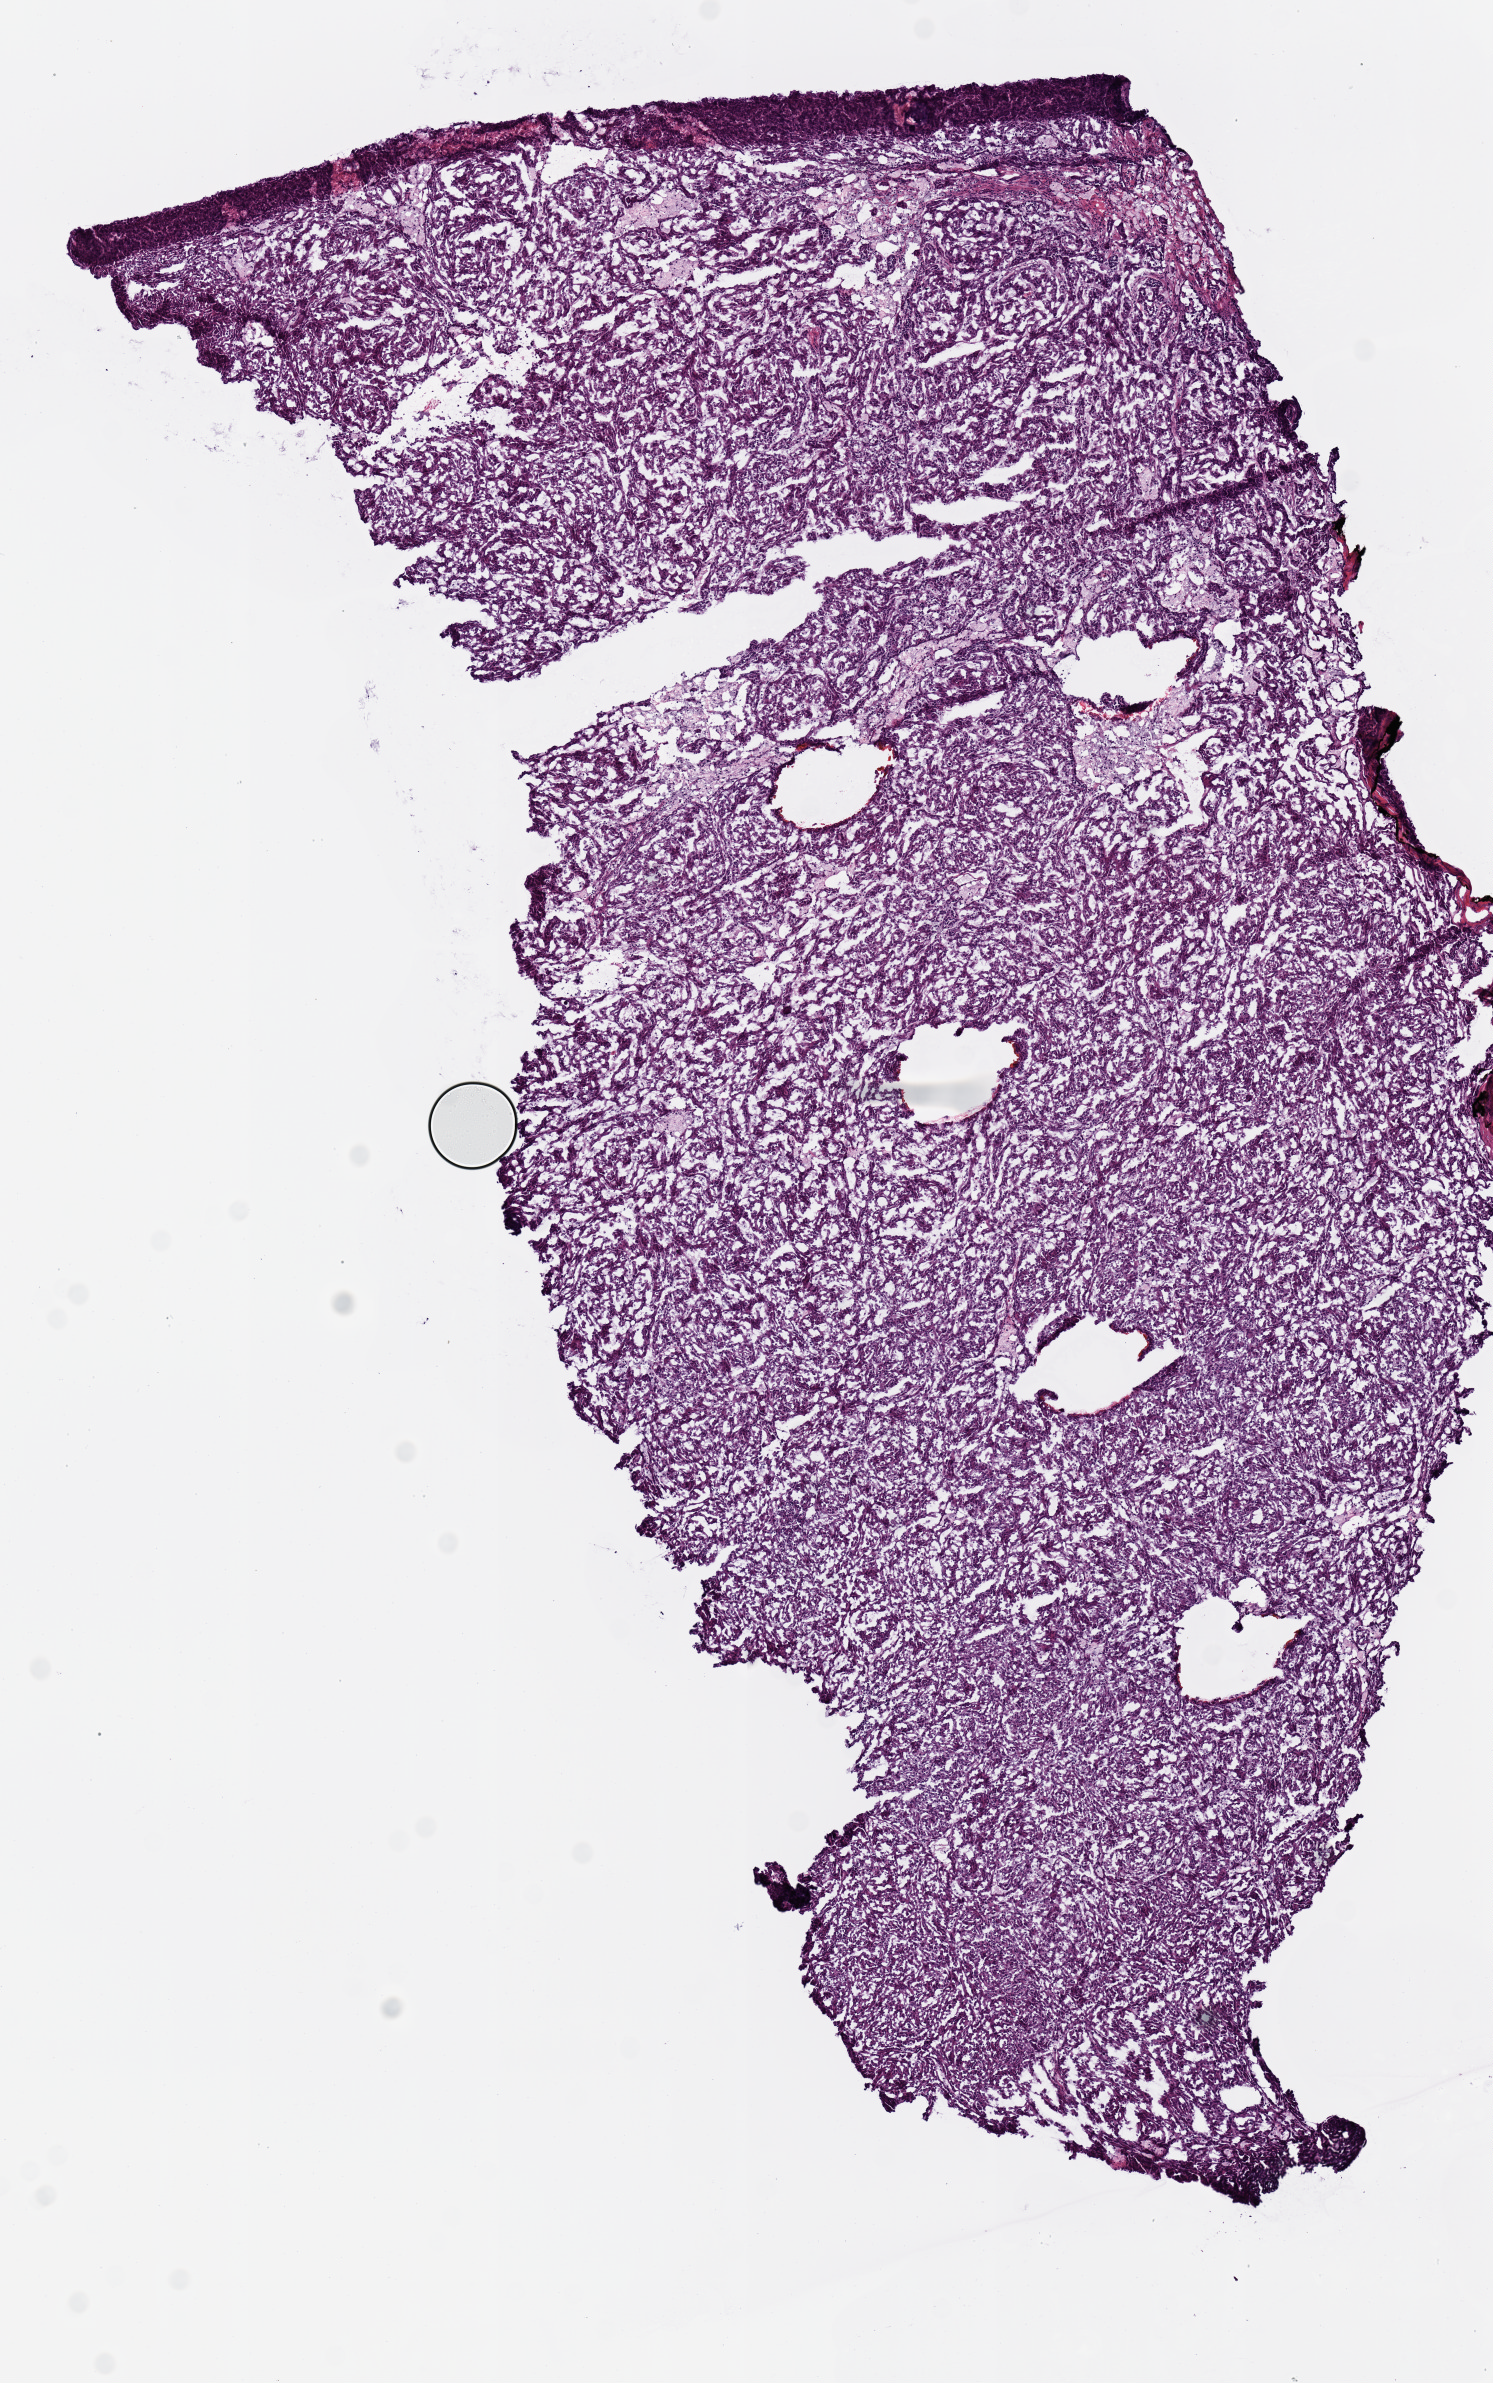
Whole-slide histology image, H&E-stained — low-resolution overview of the scanned area, about 5.9 x 9.4 mm (from a 20x scan); frozen section from the top of the tissue portion; kidney, primary tumour sample. Patient: male, age at initial diagnosis 60 years. Slide review estimates, as recorded: tumour nuclei 90%, necrosis 0%.
• AJCC pathologic stage: I
• diagnosis: Papillary adenocarcinoma, NOS